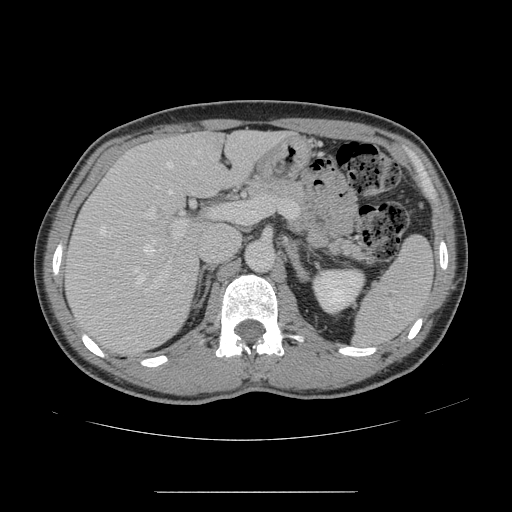
Contrast-enhanced abdominal CT, one axial slice. Position 89 of 178 along the scan axis. 120 kVp. Intravenous contrast given. Soft-tissue window (W 400 / L 40 HU). 2.5 mm slice thickness. 512 × 512 image matrix, field of view 401 × 401 mm. Male patient, age 53 years. Case-level facts recorded for this patient, not image findings: diagnosis: colorectal cancer liver metastases, imaged before liver resection; multiple liver metastases: yes; largest metastasis: 2.4 cm; disease in both lobes: no.
Outlined on this slice (expert manual segmentation):
- hepatic veins: box from (x=99, y=160) to (x=195, y=287) px
- liver: (x=68, y=132)–(x=281, y=353)
- planned liver remnant (the part of the liver to remain after resection): (x=150, y=132)–(x=282, y=194)
- portal vein (with intrahepatic branches): (x=143, y=196)–(x=267, y=288)